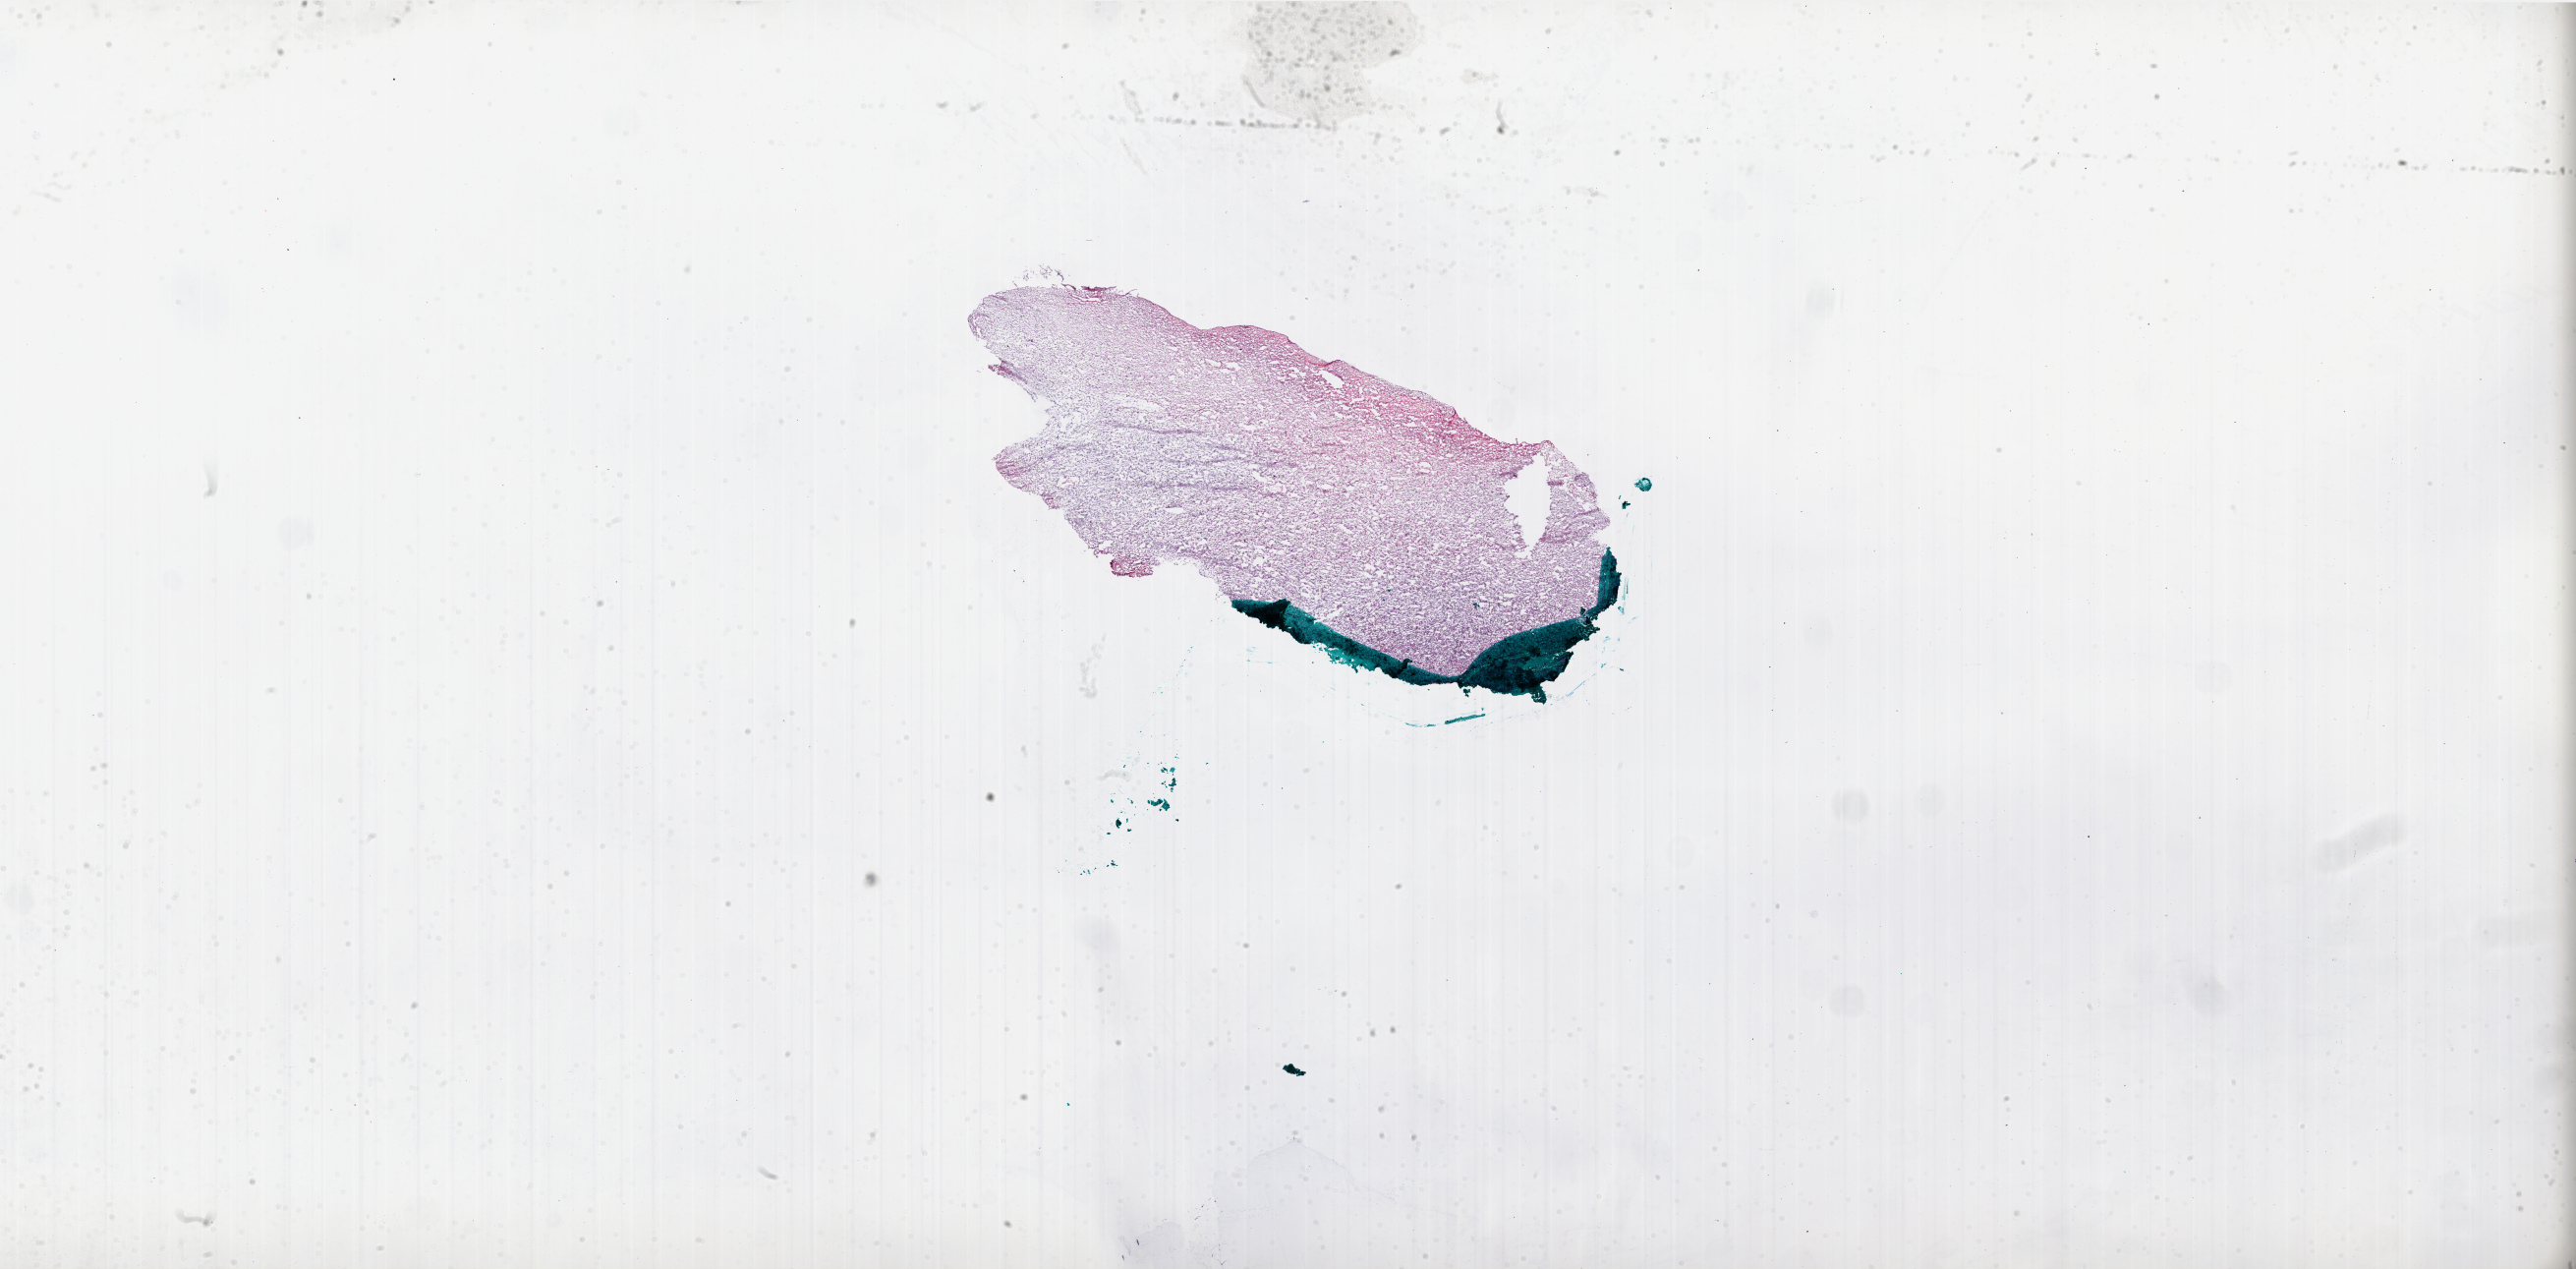
Whole-slide histology image, Hematoxylin and eosin (H&E) stained — low-resolution overview of the scanned area, about 42.0 x 20.7 mm (slide scanned at 20x), frozen section, sample: primary tumour, brain. Patient: male, age at initial diagnosis 36 years. Composition of this section per pathologist review: tumour cells 70%, tumour nuclei 90%, normal cells 0%, stromal cells 25%, necrosis 5%. Infiltration values recorded for this section: lymphocyte infiltration 0%.
Histologic diagnosis: Glioblastoma.